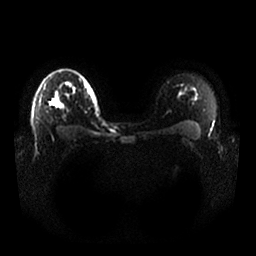
Breast MRI, one axial slice; position 21 of 25 along the scan axis; diffusion-weighted series; image 2 of 4 stored at this slice position (different b-values; order by instance number); 1.5 T; 256 × 256 image matrix. Female patient.
Structures marked on this image (manually delineated by an expert):
- tumour on diffusion-weighted imaging: bounding box [x1, y1, x2, y2] px = [50, 102, 59, 106]